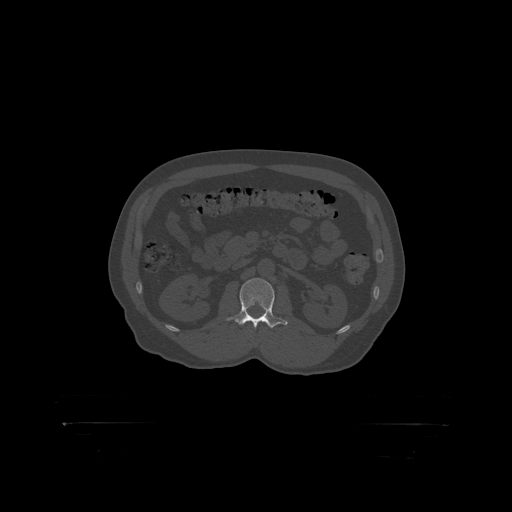
CT including the spine, one axial slice; slice 299 of 399 in the series (ordered by position); 120 kVp; bone window (W 1800 / L 400 HU); 1.25 mm slice thickness; 512 × 512 image matrix. Patient: male, 46 years. From the clinical record (not read from this slice): primary cancer: skin.
Structures marked on this image (semi-automatic segmentation, software-assisted and operator-edited):
- L2 vertebra: bounding box <237,279,275,319> (left, top, right, bottom; pixels)